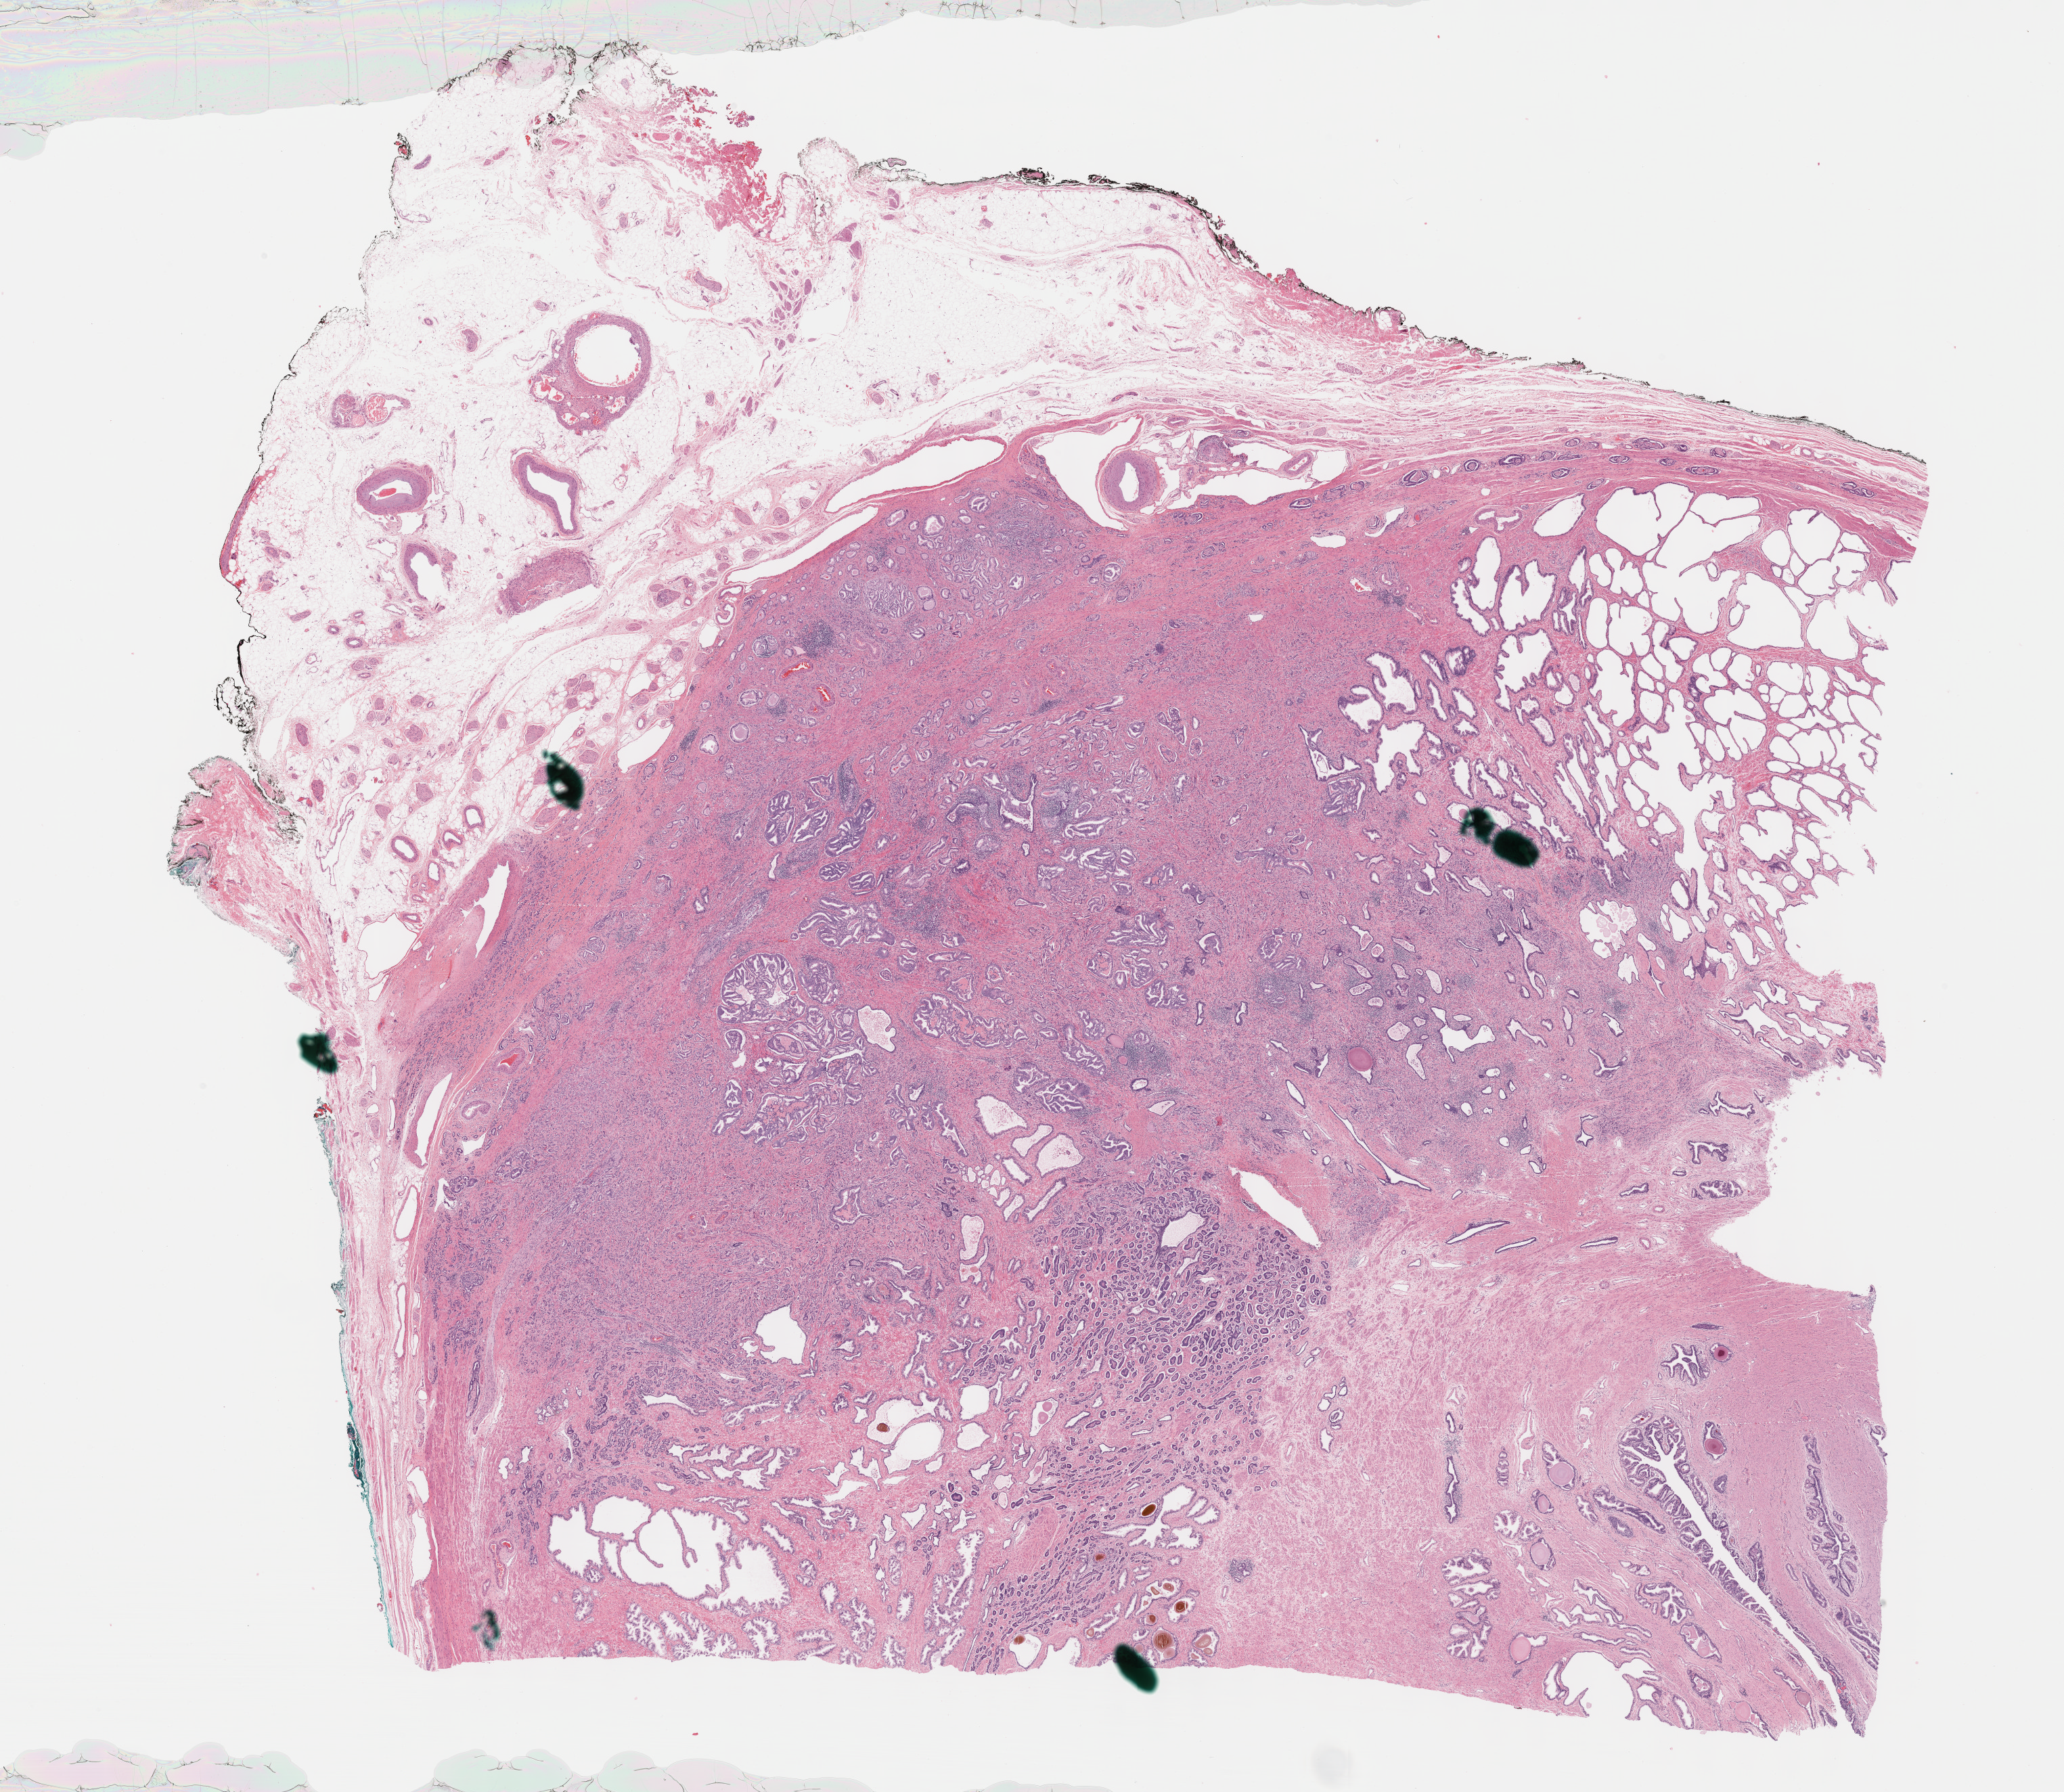
Whole-slide histology image, H&E — whole scanned area (about 24.7 x 21.4 mm) shown as a low-resolution overview, formalin-fixed paraffin-embedded (FFPE) diagnostic section, prostate, primary tumour sample. Patient: male, age at initial diagnosis 56 years. Gleason score: 8 (3+5).
Pathologic diagnosis: Adenocarcinoma, NOS. Lymph nodes positive (case pathology): 0 of 12 examined.